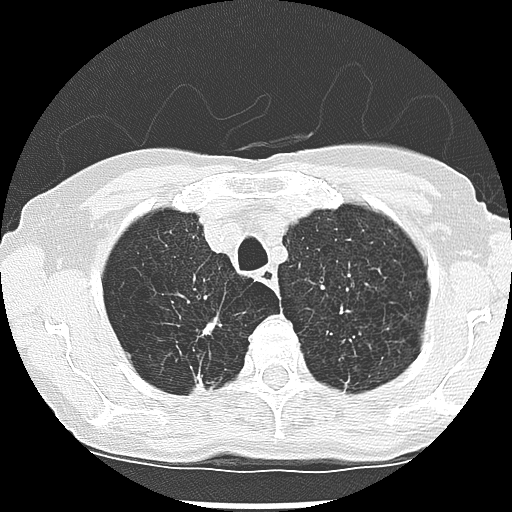
Low-dose screening chest CT, one axial slice; position 225 of 265 along the scan axis; reconstruction kernel LUNG; 120 kVp; lung window (W 1500 / L -600 HU); 2.5 mm slice thickness; 512 × 512 image matrix, field of view 300 × 300 mm.
Structures marked on this image (outlined manually by an expert reader):
- lesion 1 (nodule, upper lobe of right lung): bounding box [x1, y1, x2, y2] px = [194, 375, 205, 393]
- lesion 2 (tumor, upper lobe of right lung): [203, 322, 217, 335]